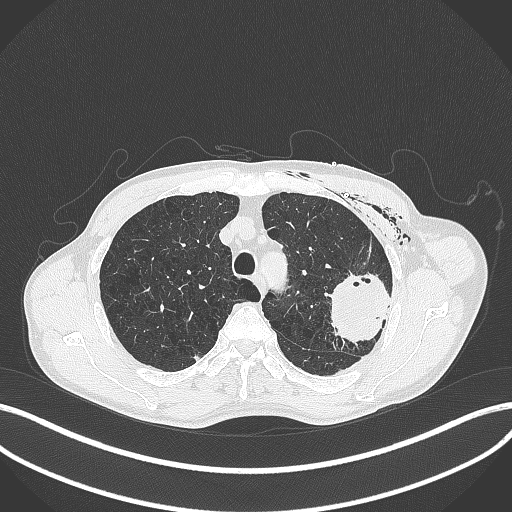
Chest CT, one axial slice. Position 315 of 457 along the scan axis. Lung window (W 1500 / L -600 HU). 1 mm slice thickness. 512 × 512 image matrix, field of view 400 × 400 mm. Patient: male, 58 years. From the clinical record (not read from this slice): clinical TNM (as recorded): T3 N0 M0.
Annotated regions visible in this slice (rectangle marked by the reading radiologist):
- lung tumour (recorded histology: adenocarcinoma): bounding box (x1, y1, x2, y2) in pixels: (323, 271, 393, 346)